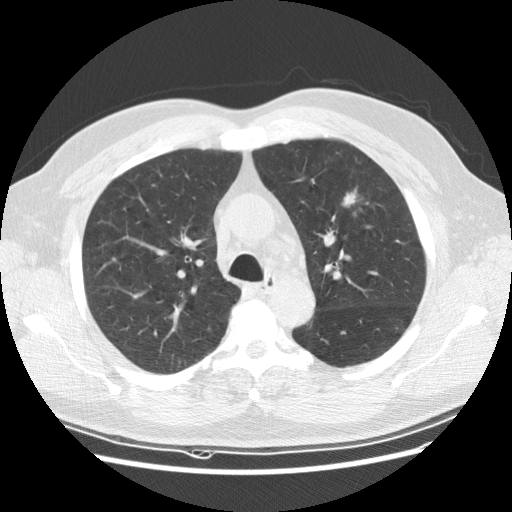
Low-dose screening chest CT, axial slice, baseline annual screen, lung window (W 1500 / L -600 HU), 512 × 512 image matrix, field of view 367 × 367 mm. Male participant, aged 65 years at enrolment. Current smoker at enrolment.
- Lesion marked by an expert reader, bounding box <324,181,379,229> (left, top, right, bottom; pixels).
- The screening reader recorded 2 non-calcified nodules or masses ≥4 mm on this exam (left upper lobe, right upper lobe); which of them this box marks is not recorded.